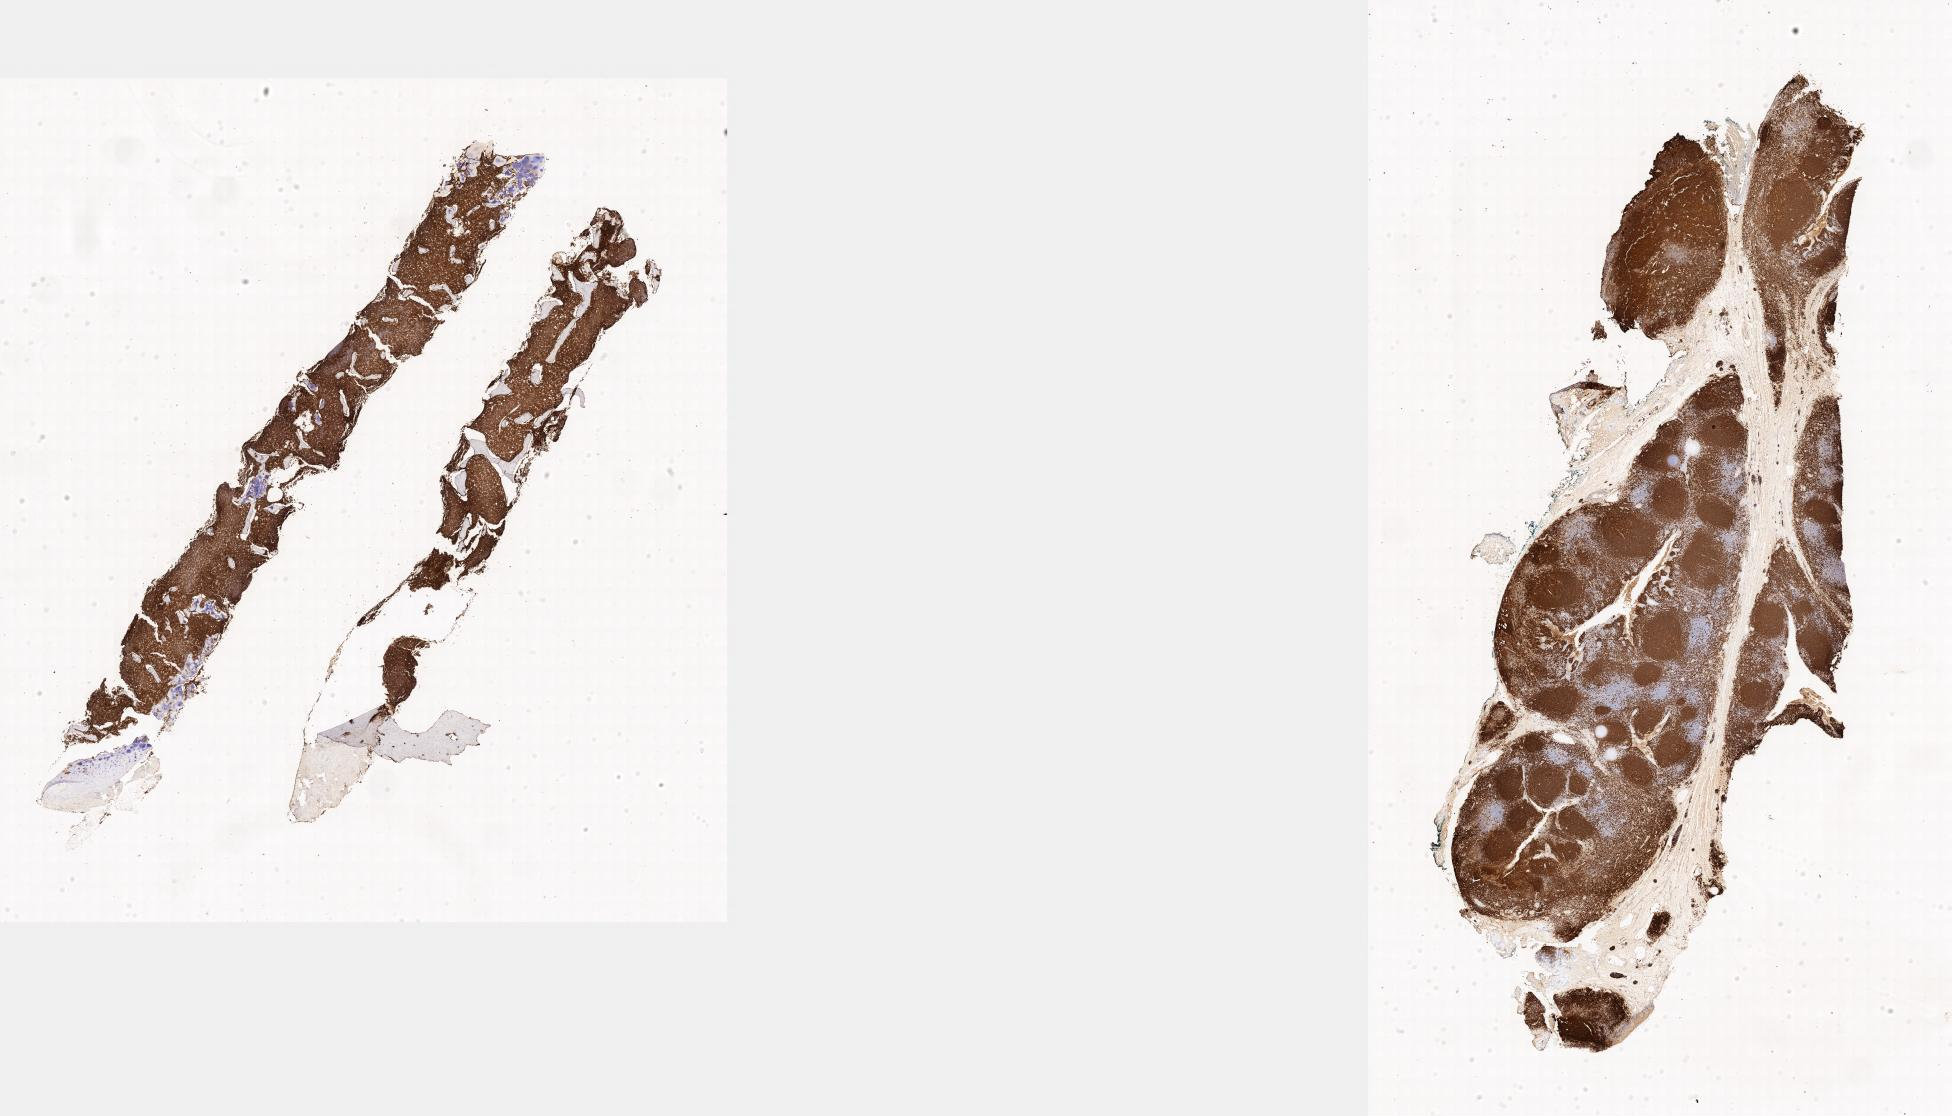
IHC for CD20, whole-slide image — shown as a low-resolution overview of the whole scanned area, tumor tissue, site: bone marrow. Male patient, 16 years old.
Histologic diagnosis: Burkitt lymphoma, NOS.